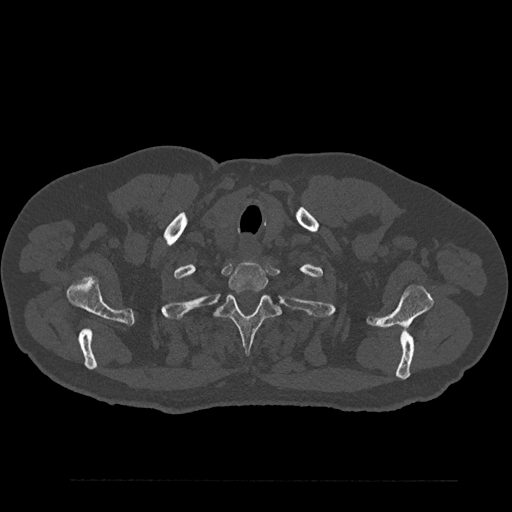
CT including the spine, one axial slice; bone window (W 1800 / L 400 HU); 512 × 512 image matrix, field of view 430 × 430 mm. Male patient, age 61 years. Case-level facts recorded for this patient, not image findings: primary cancer: prostate.
Outlined on this slice (semi-automatically segmented with operator editing):
- T1 vertebra: bounding box (x1, y1, x2, y2) in pixels: (228, 262, 268, 292)
- T2 vertebra: (216, 295, 280, 354)
- T3 vertebra: (209, 334, 211, 336)